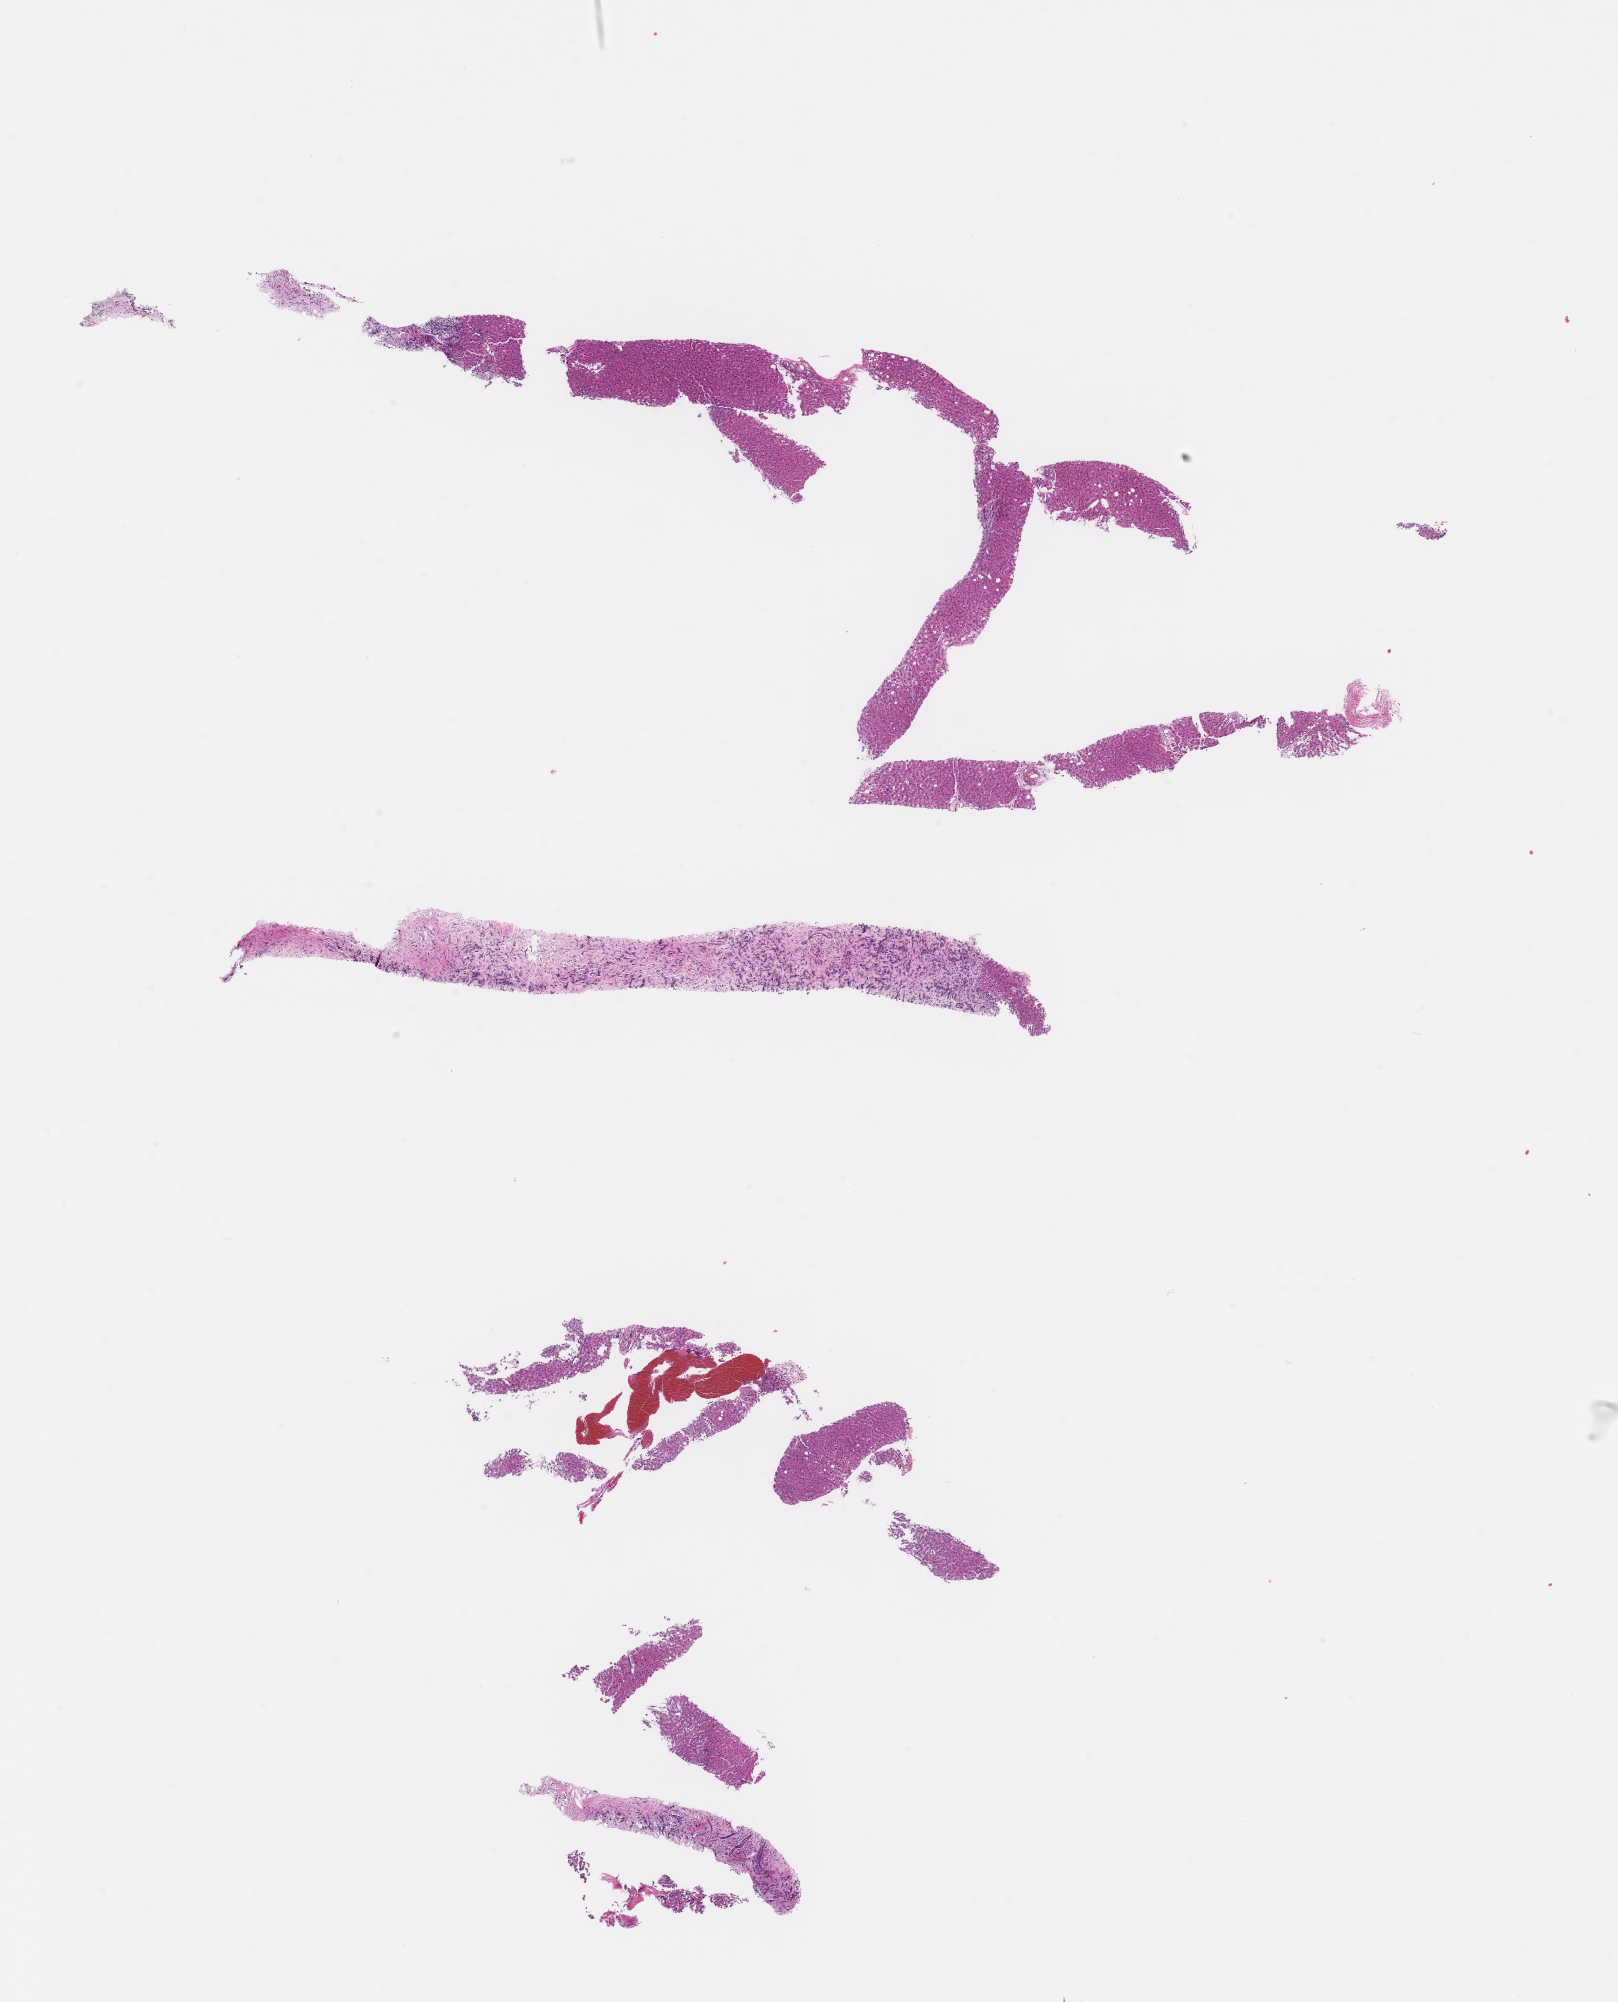
H&E whole-slide image — a low-resolution overview of the entire scanned area, about 13.1 x 16.2 mm, FFPE section, archival tissue. Patient: female.
• this section: metastasis (sampled organ not recorded)
• patient diagnosis (primary): Invasive Breast Carcinoma